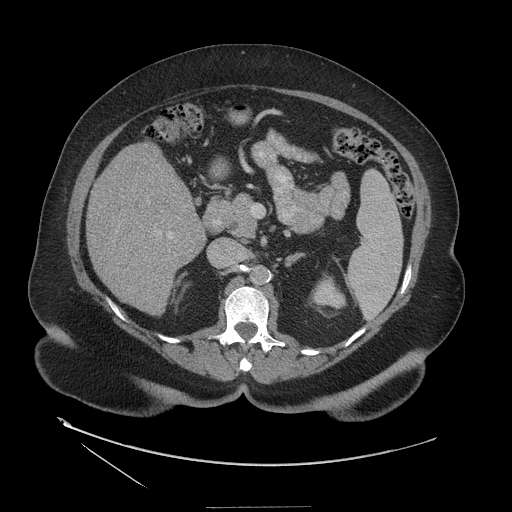
Contrast-enhanced abdominal CT (liver protocol), one axial slice. Position 61 of 127 along the scan axis. Reconstruction kernel STANDARD. Soft-tissue window (W 400 / L 40 HU). 512 × 512 image matrix, field of view 480 × 480 mm. Case-level facts recorded for this patient, not image findings: diagnosis: hepatocellular carcinoma (patient treated with transarterial chemoembolisation; whether this scan precedes or follows treatment is not stated here); TNM stage (as recorded): Stage-II; Child-Pugh class: A; tumour differentiation: well differentiated.
Annotated regions visible in this slice (semi-automatic segmentation, software-assisted and operator-edited):
- liver parenchyma outside the tumour (the mass and vessels are separate outlines, so this box may not span the whole liver): bounding box <86,142,206,314> (left, top, right, bottom; pixels)
- liver vessels: <169,236,172,238>